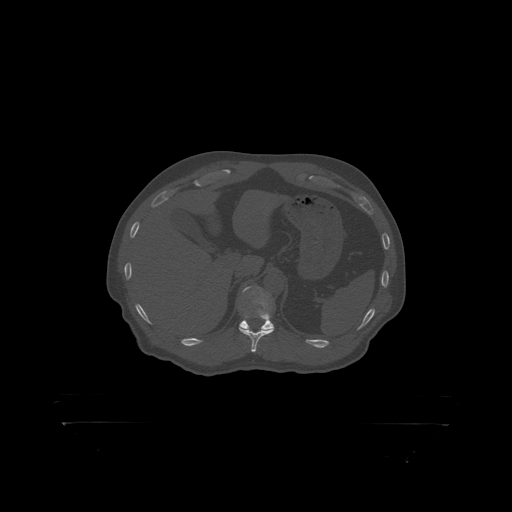
CT including the spine, one axial slice; slice 368 of 399 in the series (ordered by position); reconstruction kernel STANDARD; 120 kVp; bone window (W 1800 / L 400 HU); 512 × 512 image matrix, field of view 650 × 650 mm. Male patient, age 46 years. Case-level facts recorded for this patient, not image findings: primary cancer: skin.
Outlined on this slice (semi-automatically segmented with operator editing):
- T12 vertebra: bounding box [x1, y1, x2, y2] px = [241, 287, 273, 318]